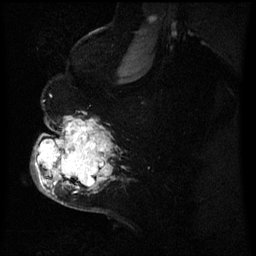
Breast MRI (dynamic contrast-enhanced), one sagittal slice; position 43 of 60 along the scan axis; dynamic contrast-enhanced series, image 2 of 3 at this slice position (ordered by acquisition); 1.5 T; TE 4.2 ms, TR 8 ms; 256 × 256 image matrix, field of view 200 × 200 mm. Female patient, age 50 years.
Annotated regions visible in this slice (semi-automatically segmented with operator editing):
- analysis volume of interest (the breast-tissue region the enhancement analysis was run in; not a lesion): box from (x=35, y=120) to (x=111, y=199) px
- tumour enhancement mask (voxels above the 70 % enhancement threshold inside the analysis volume of interest): (x=38, y=120)–(x=104, y=189)